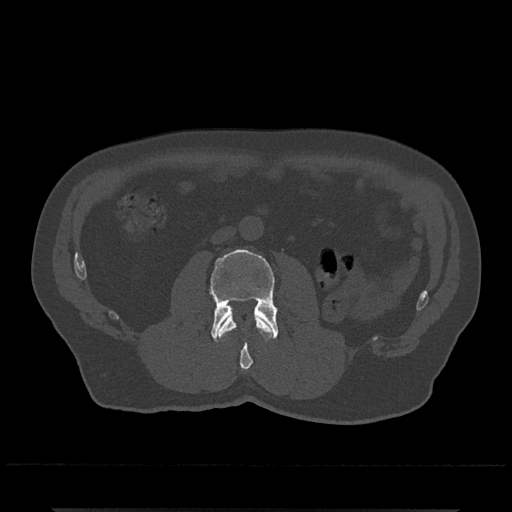
CT including the spine, one axial slice; slice 245 of 797 in the series (ordered by position); reconstruction kernel Br40s/3; 120 kVp; bone window (W 1800 / L 400 HU); 0.5 mm slice thickness; 512 × 512 image matrix, field of view 393 × 393 mm. Male patient, age 67 years. From the clinical record (not read from this slice): primary cancer: prostate.
Annotated regions visible in this slice (semi-automatically segmented with operator editing):
- L2 vertebra: bounding box [x1, y1, x2, y2] px = [218, 315, 272, 370]
- L3 vertebra: [210, 249, 279, 342]